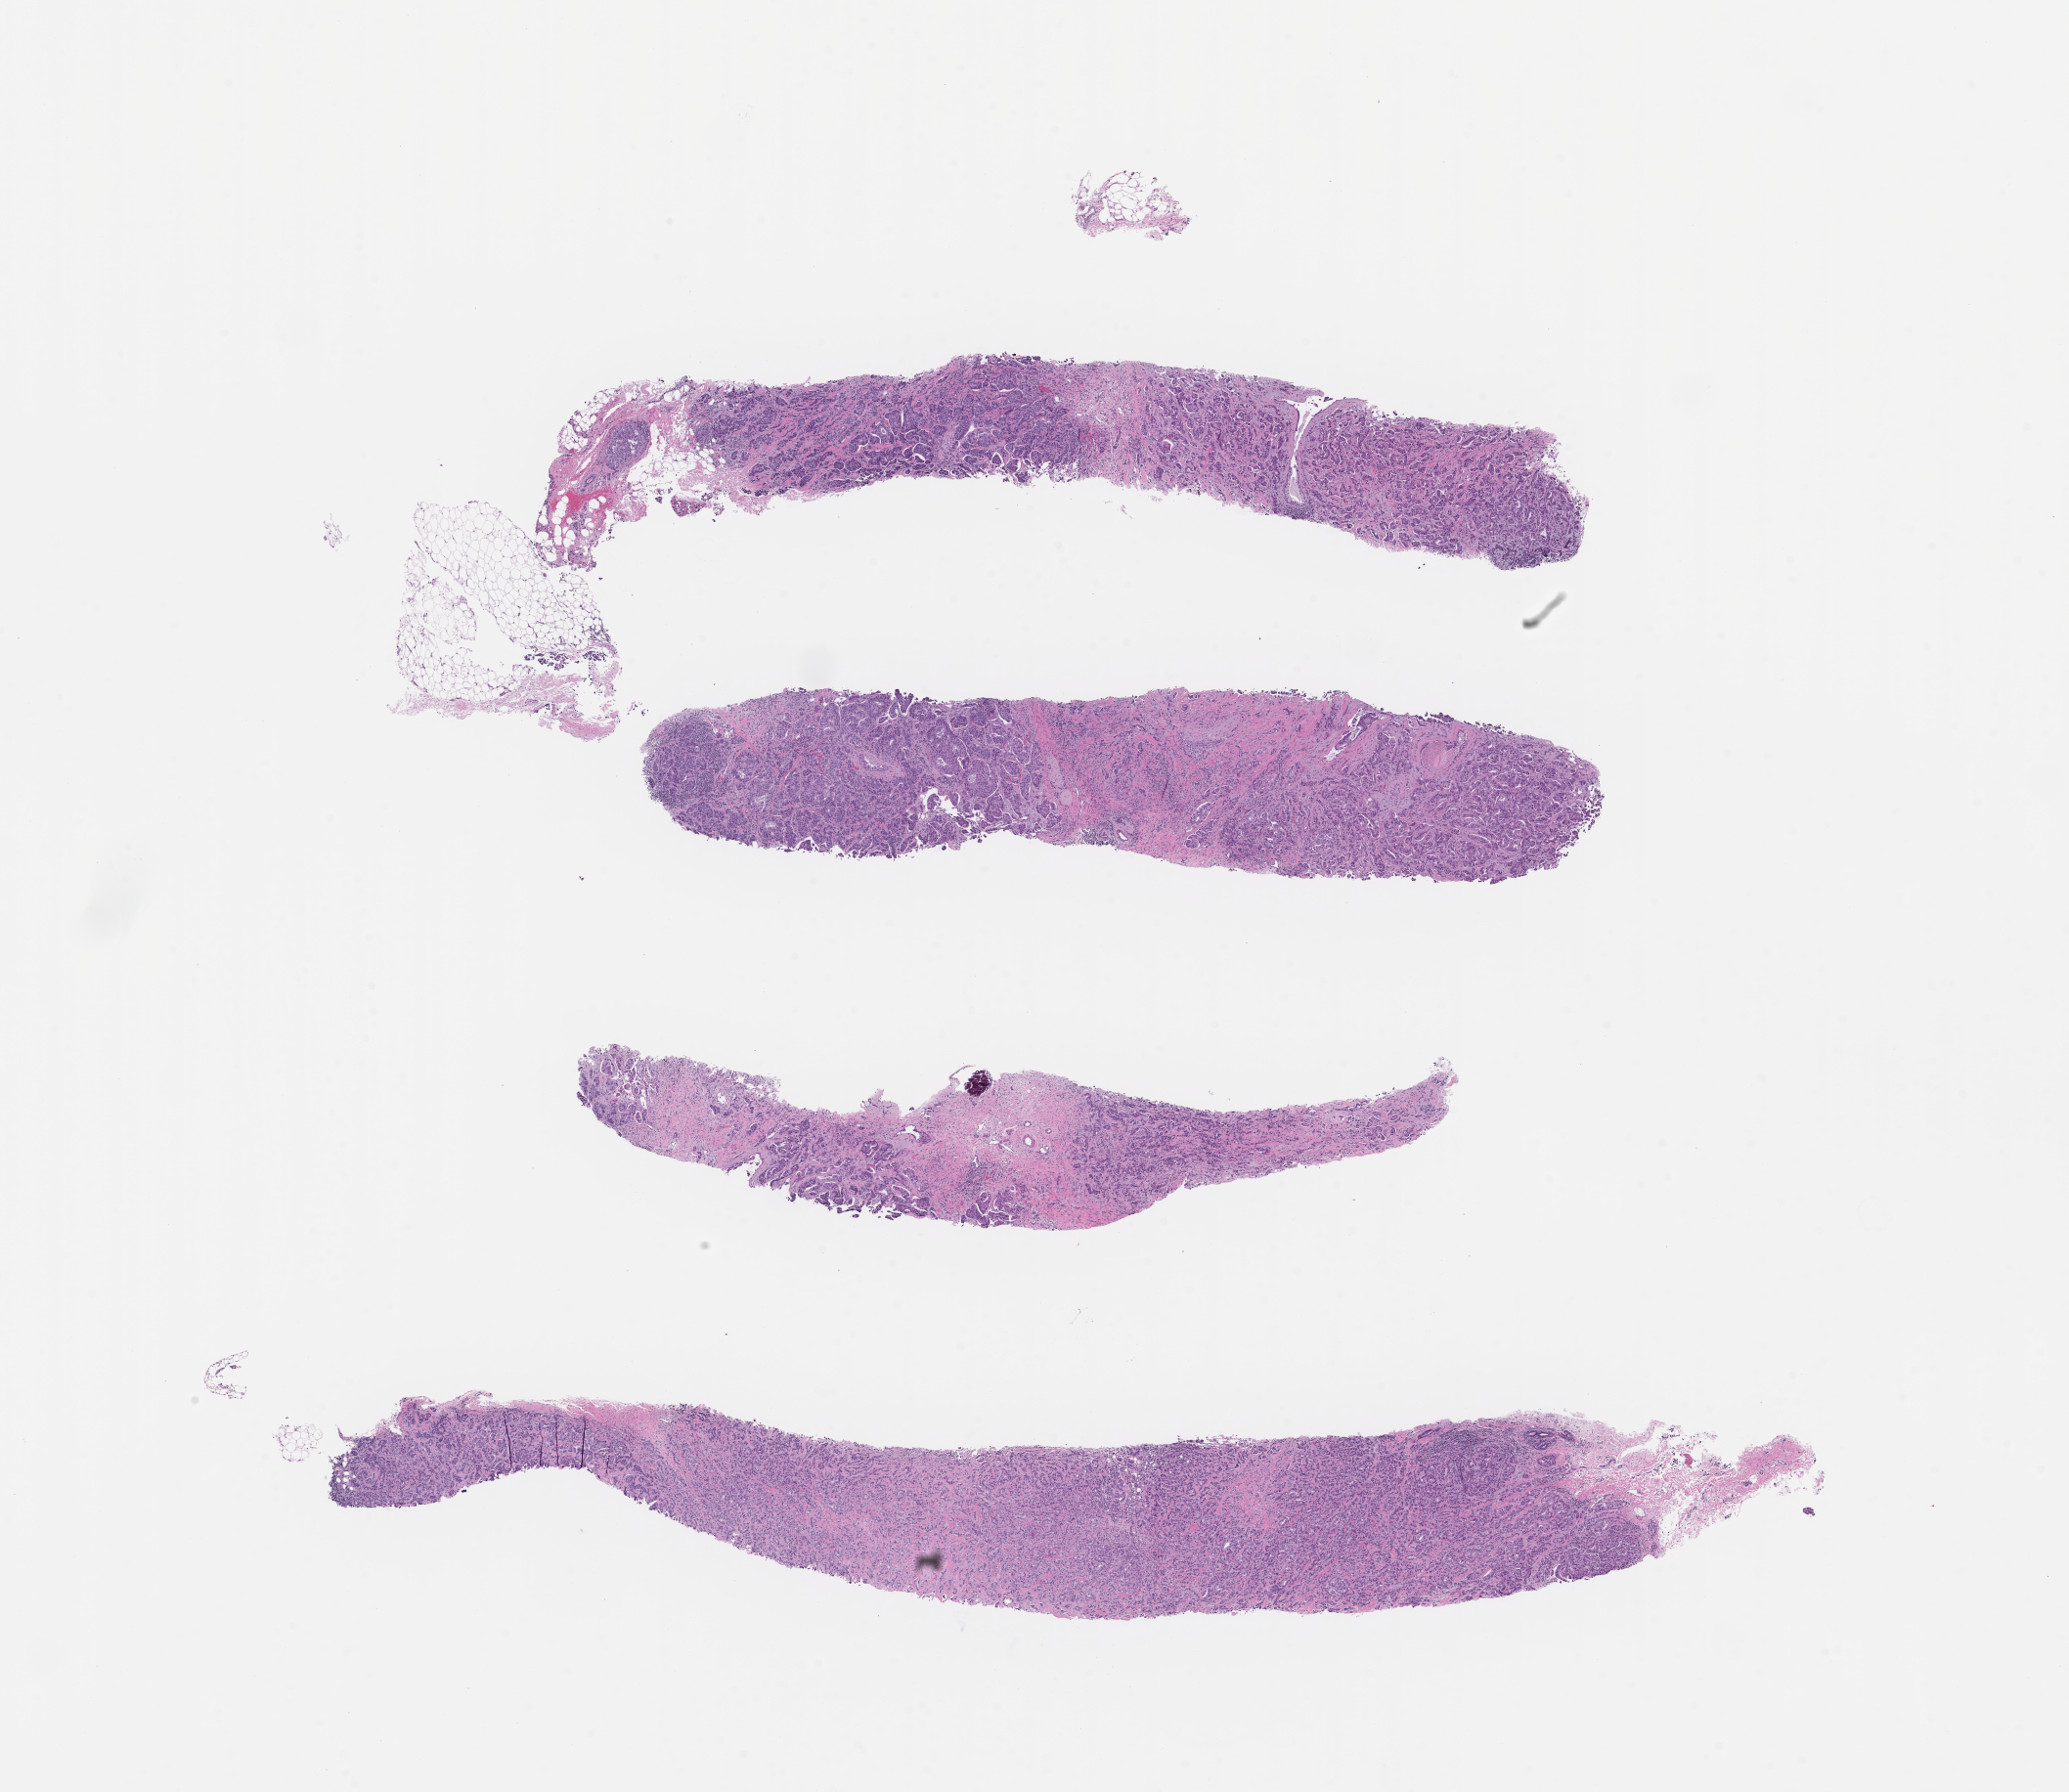
Whole-slide image, H&E stain — a low-resolution overview of the entire scanned area, about 17.1 x 14.8 mm. FFPE section. Site: breast. Specimen time point: archival tissue. Patient: female.
* this section: primary tumor
* diagnosis: Invasive Breast Carcinoma